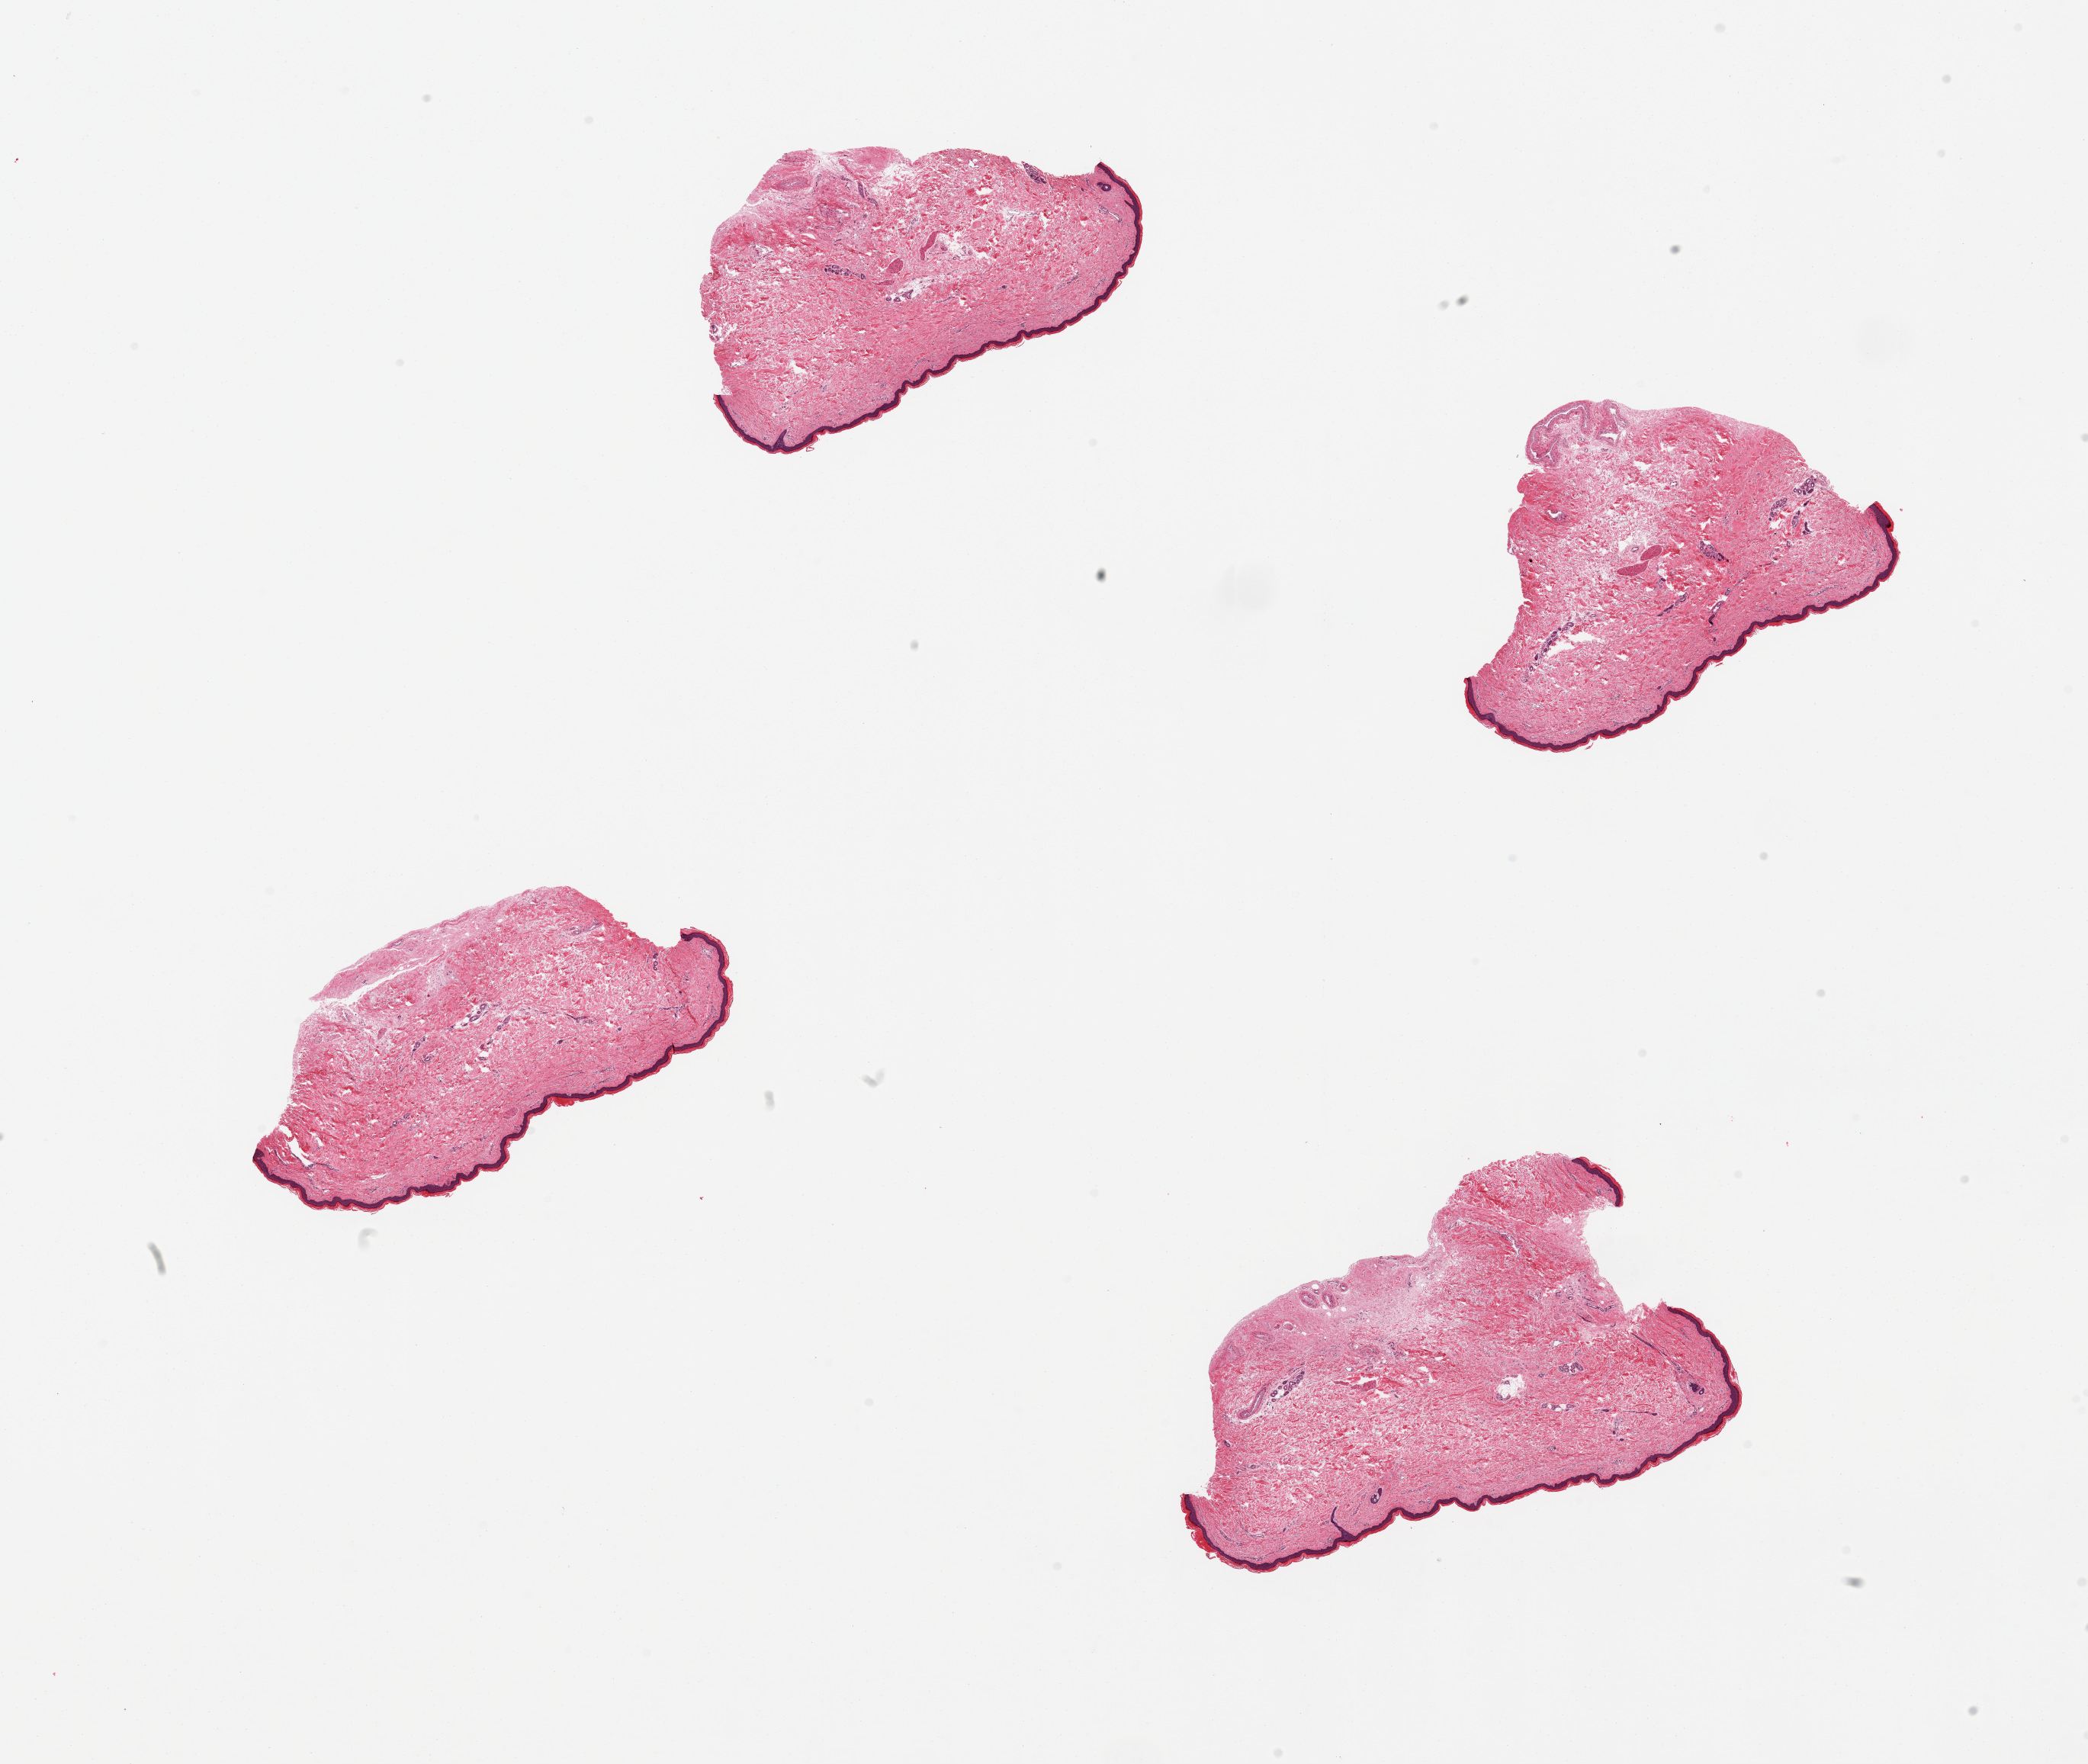
Whole-slide image, haematoxylin and eosin stain, low-resolution overview of the scanned area, about 21.7 x 18.3 mm, PAXgene-fixed, paraffin-embedded tissue, target tissue: skin of lower leg, tissue donor sample. Donor sex: female.
* pathologist's review note for this sample: 4 pieces; well trimmed, epidermis measures 36 microns